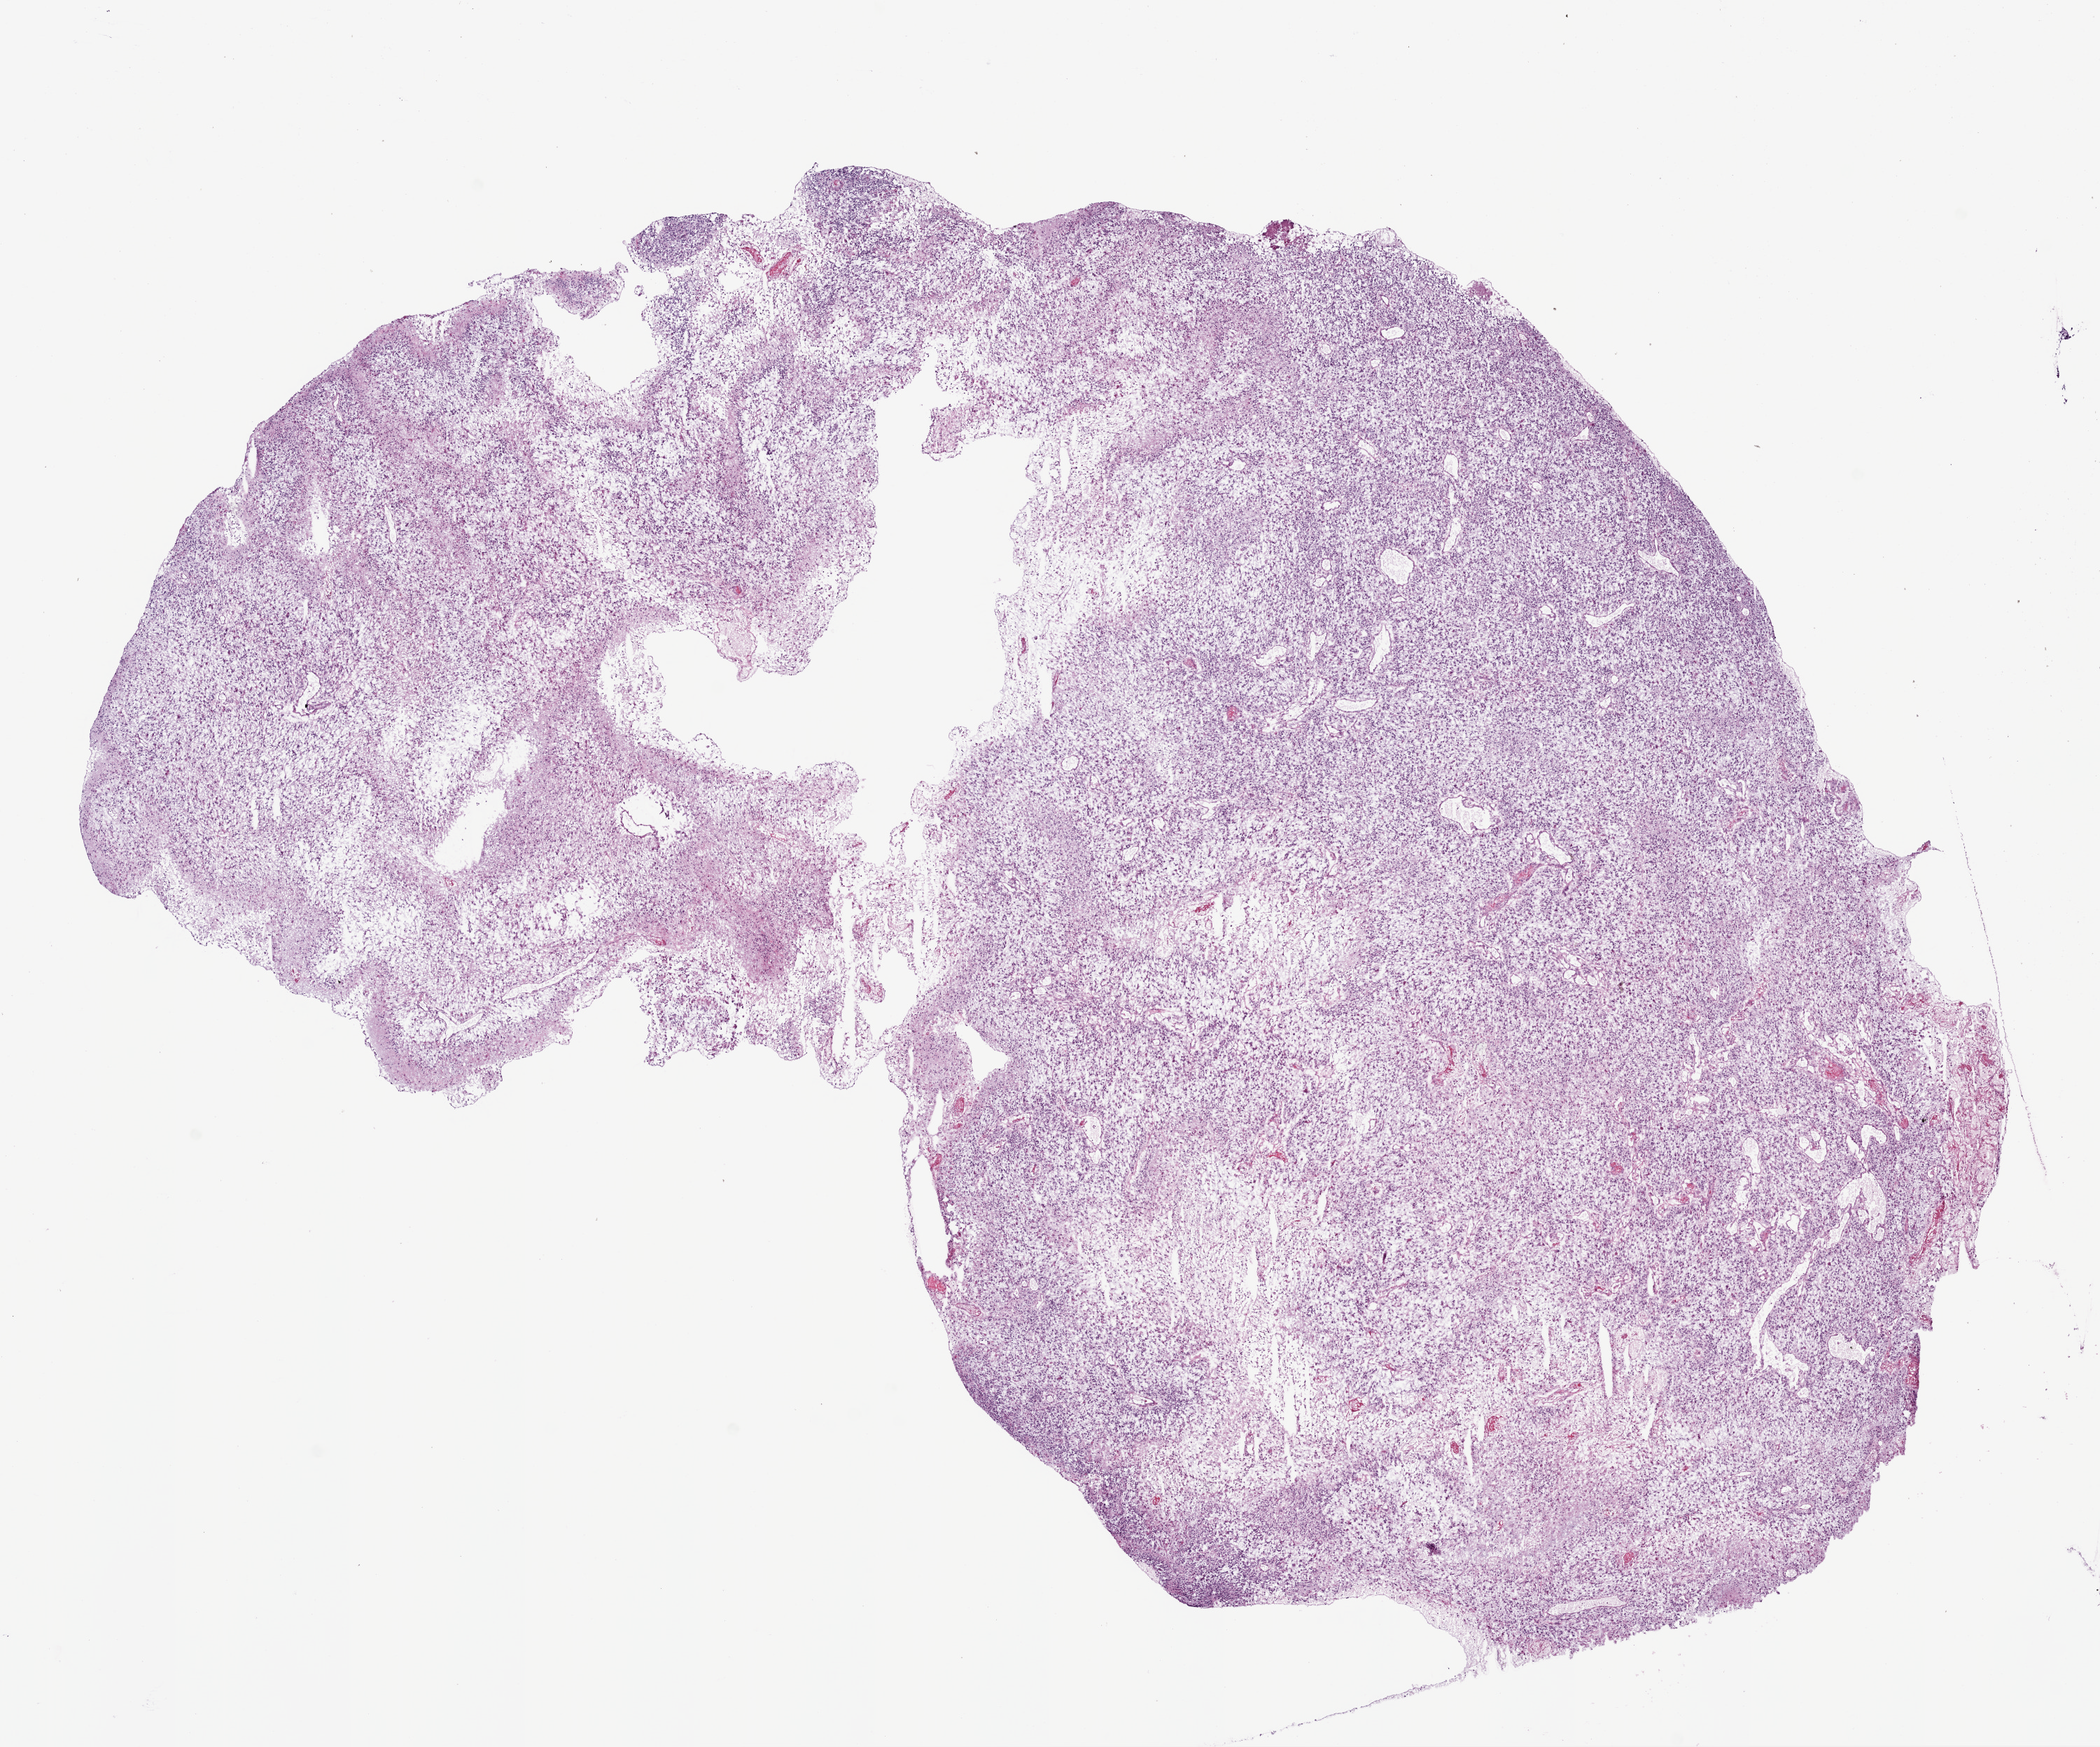
Whole-slide histology image, H&E — low-resolution overview of the scanned area, about 12.0 x 10.0 mm. Frozen section. Primary tumour sample from the brain. Male patient; age at initial diagnosis 59 years. Slide review estimates, as recorded: tumour cells 85%, tumour nuclei 80%, normal cells 0%, stromal cells 0%, necrosis 15%.
• diagnosis: Glioblastoma